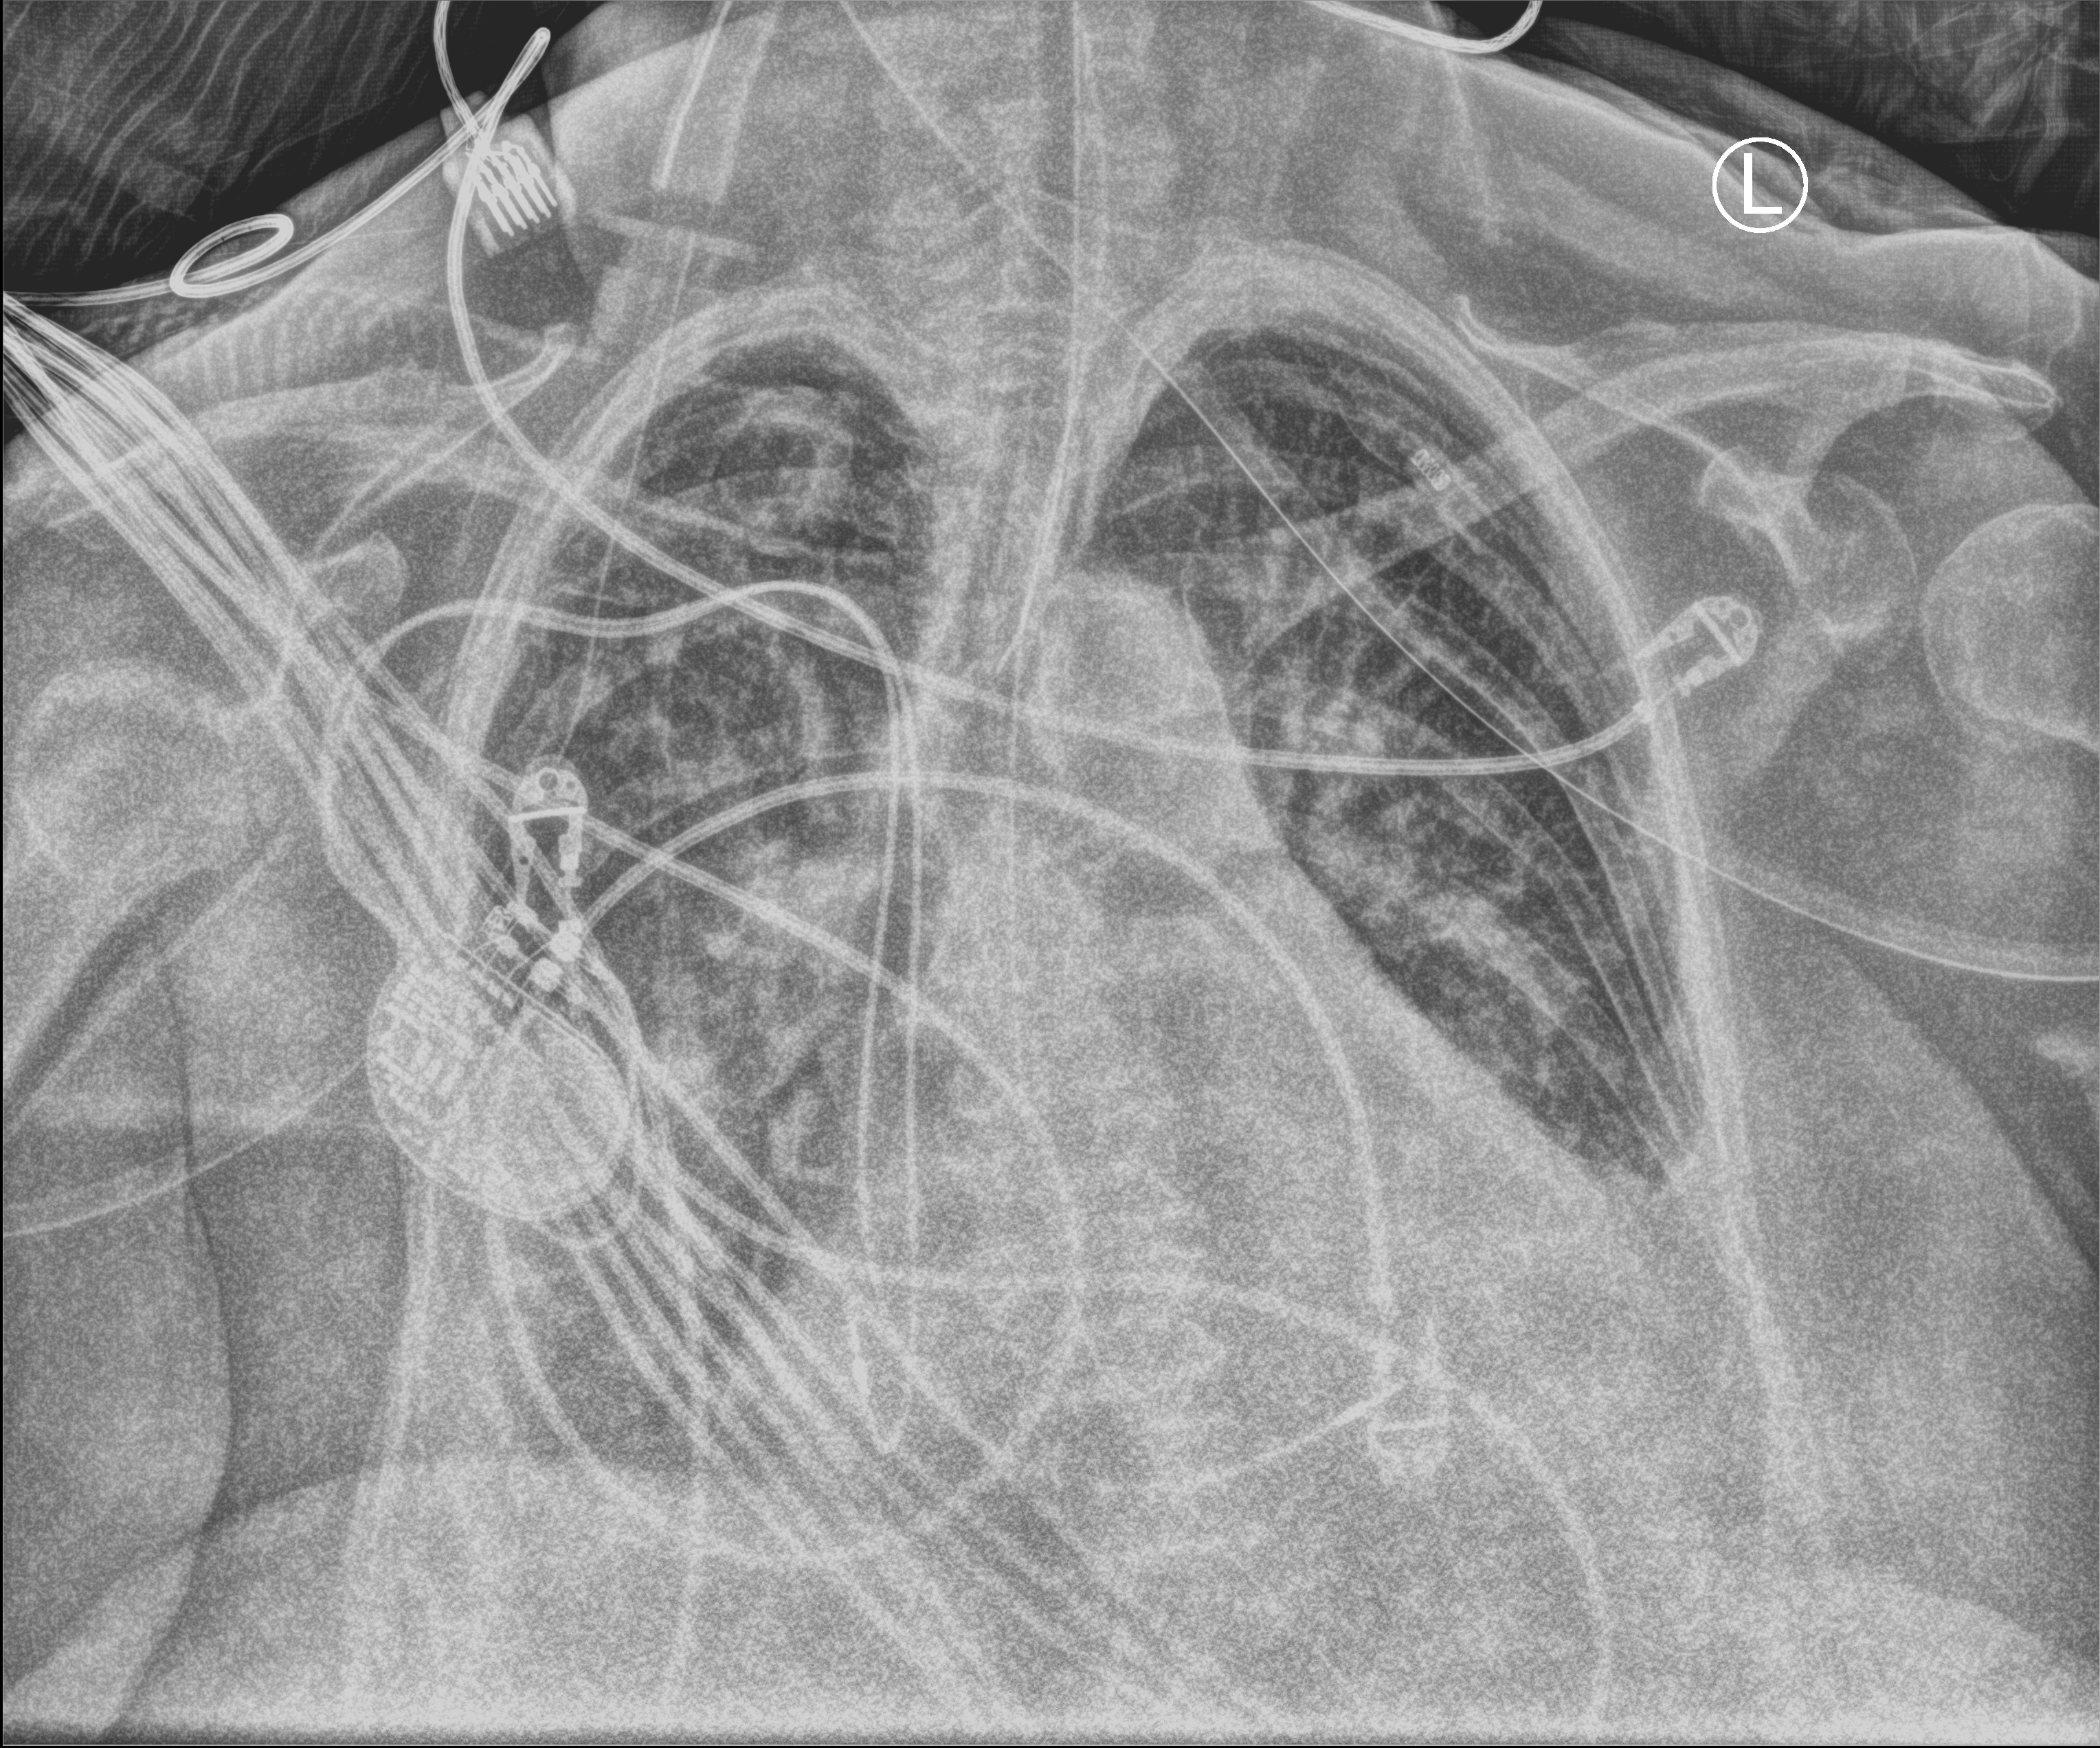
Bedside chest radiograph (computed radiography), anteroposterior (AP) projection. Female patient hospitalised with COVID-19, age 75–90 years.
Hospital-stay facts (about this admission, not read from this image; timing relative to this image not recorded):
- admitted to intensive care during this hospital stay: yes
- smoking status (admission record): former